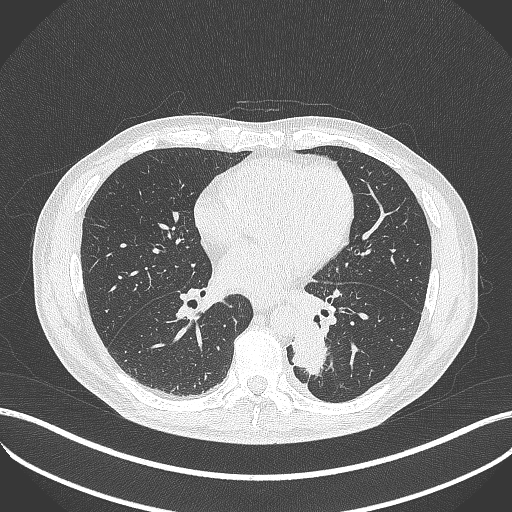
Chest CT, one axial slice; slice 178 of 451 in the series (ordered by position); lung window (W 1500 / L -600 HU); 512 × 512 image matrix, field of view 400 × 400 mm. Male patient, age 72 years. Case-level facts recorded for this patient, not image findings: clinical TNM (as recorded): T2b N0 M1.
Outlined on this slice (bounding box drawn by a radiologist):
- lung tumour (recorded histology: adenocarcinoma): box from (x=286, y=316) to (x=330, y=379) px